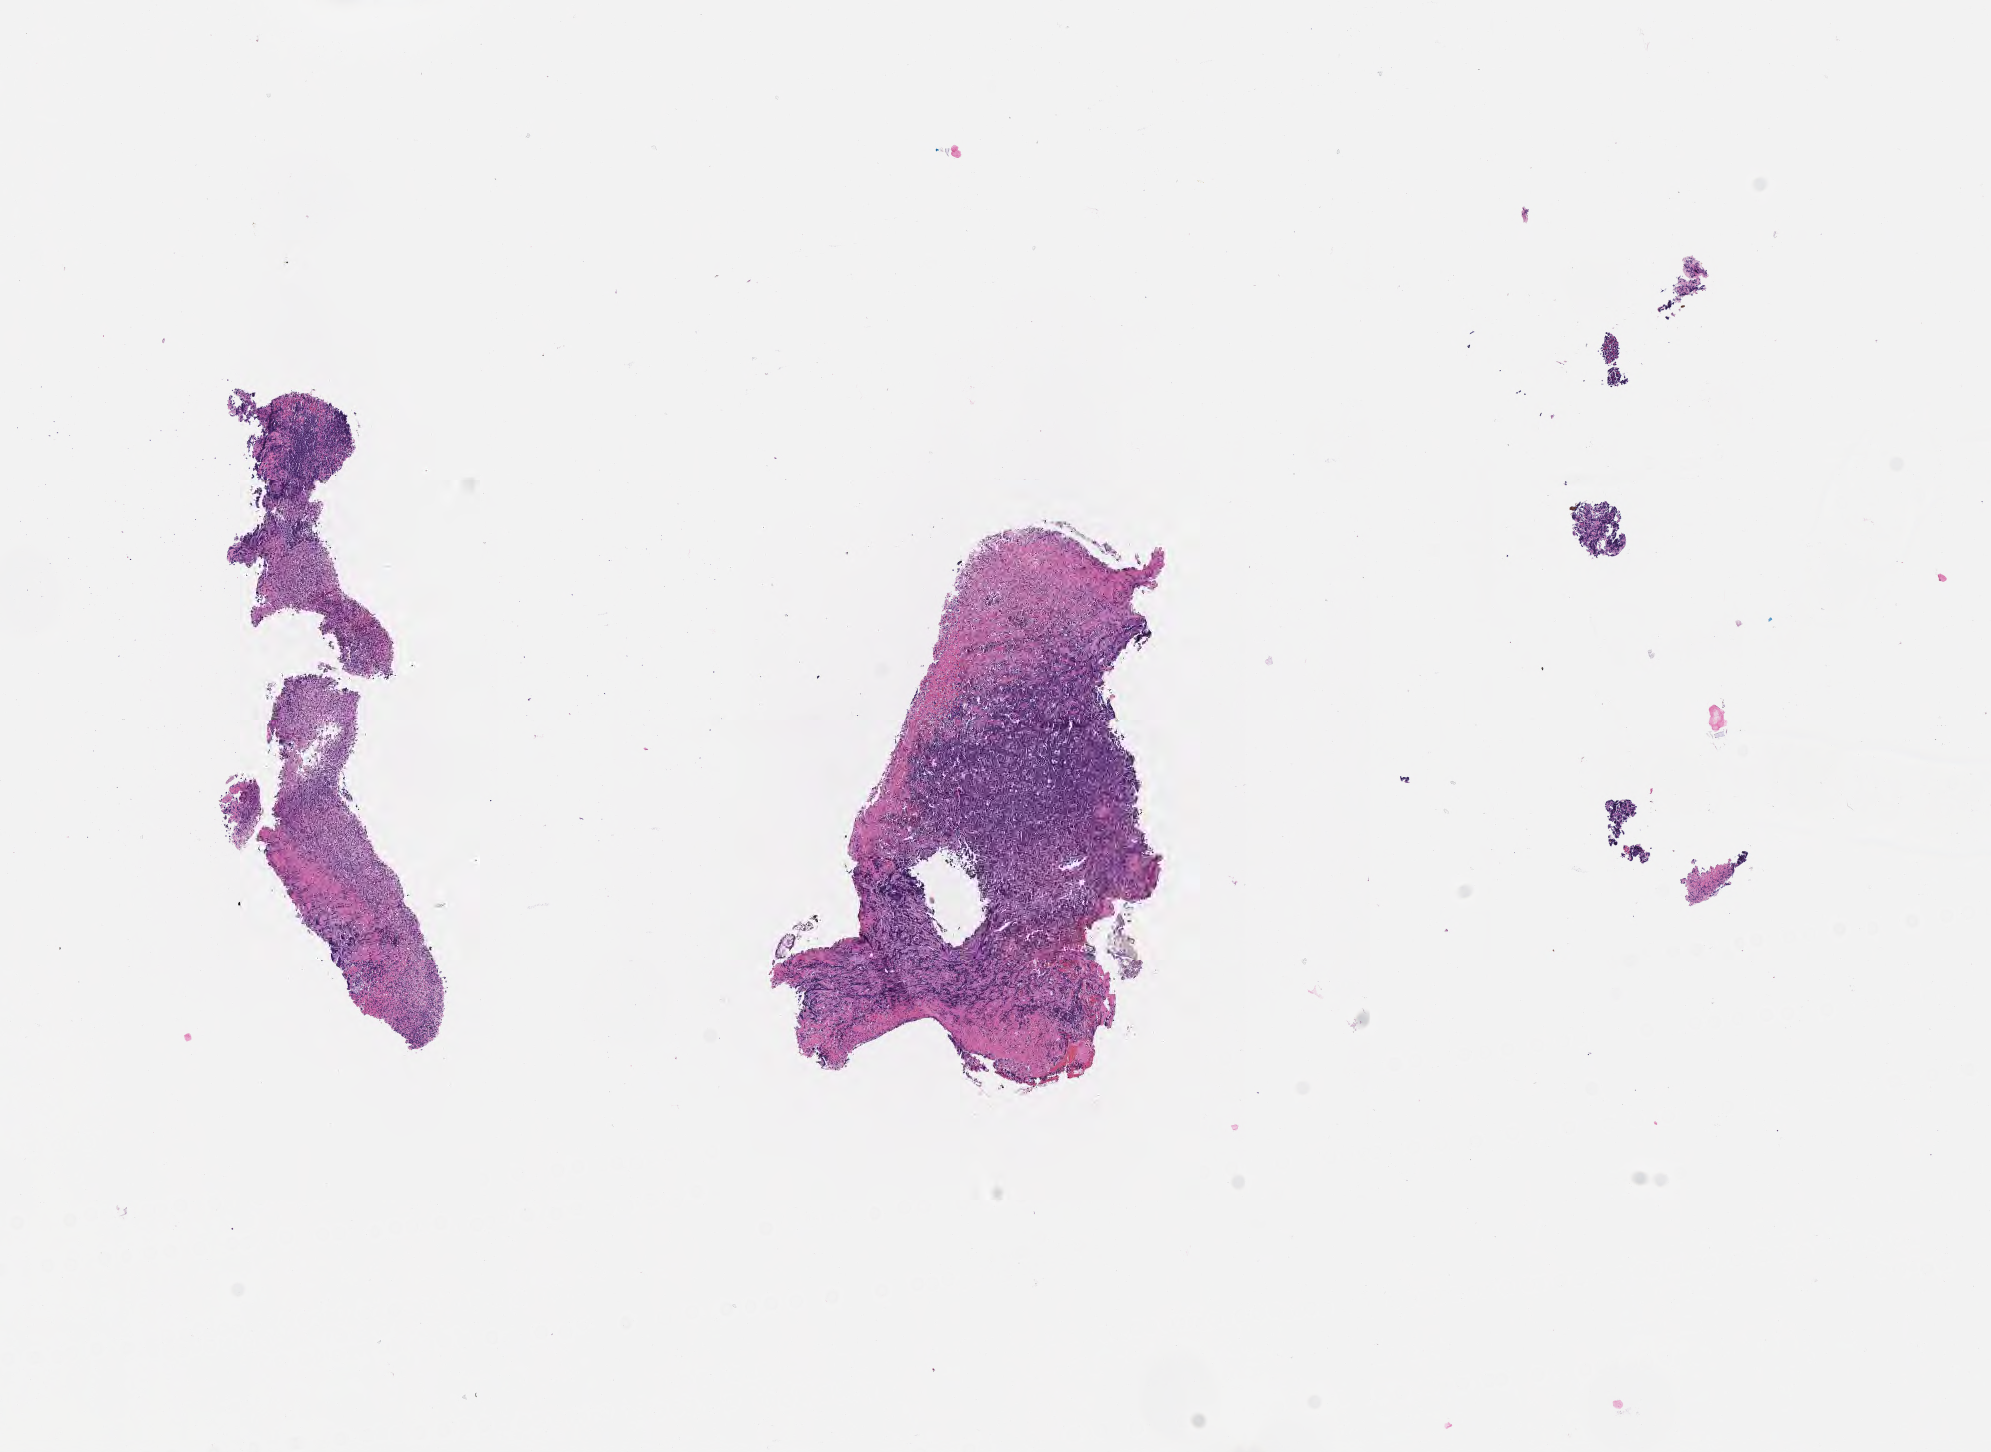
Digitized hematoxylin and eosin (H&E)-stained section, a low-resolution overview of the entire scanned area, about 8.1 x 5.9 mm, specimen: tumor tissue, site: colon. Male patient, aged 28.
Diagnosis: Burkitt lymphoma, NOS.